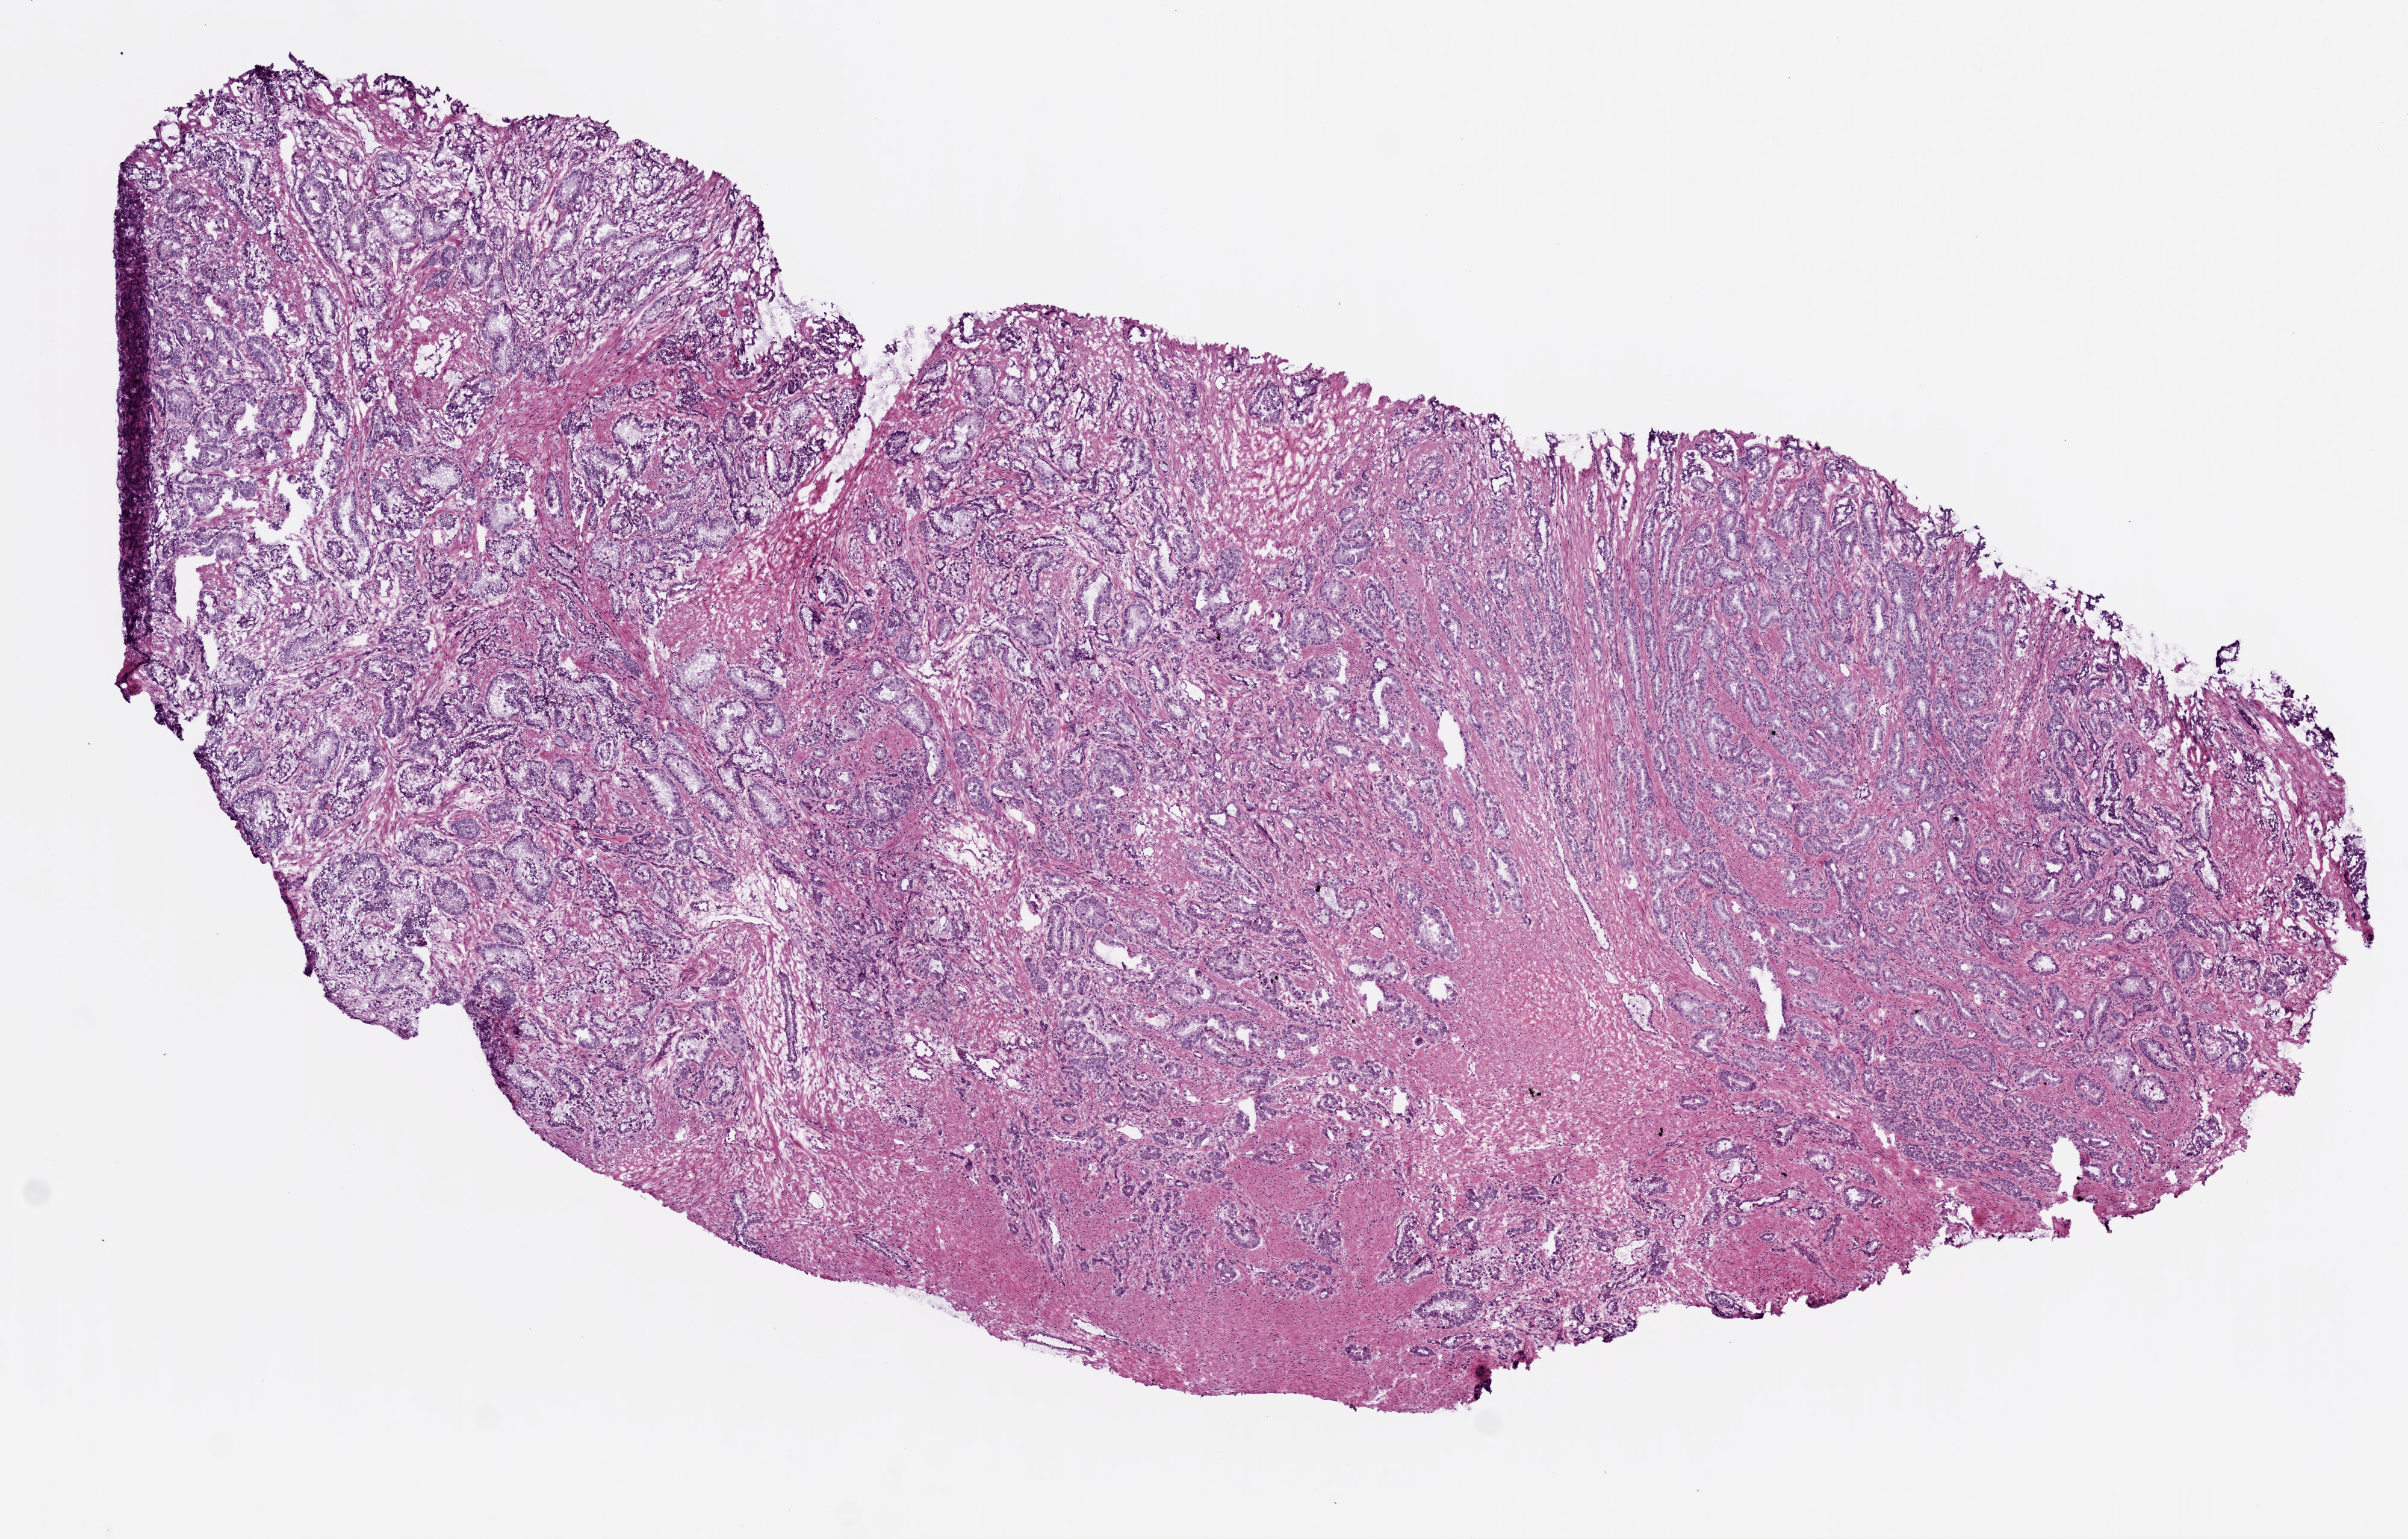
Digitized H&E tissue section (whole slide) — whole scanned area (about 8.0 x 5.1 mm) shown as a low-resolution overview. Frozen section from the top of the tissue portion. Sample: primary tumour, prostate. Male patient; age at initial diagnosis 63 years. Composition of this section per pathologist review: tumour cells 65%, tumour nuclei 70%.
Diagnosis: Acinar cell carcinoma (prostate gland).